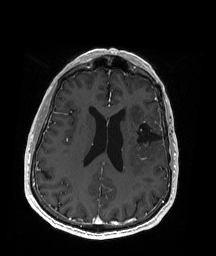
Brain MRI from a brain-tumour surgery series, one axial slice. Position 77 of 192 along the scan axis. T1-weighted post-contrast. 1 mm slice thickness. 216 × 256 image matrix, field of view 211 × 250 mm. From the clinical record (not read from this slice): histopathology: Oligodendroglioma; WHO grade: 2.
Outlined on this slice (outlined manually by an expert reader):
- previous resection cavity: box from (x=132, y=121) to (x=163, y=148) px